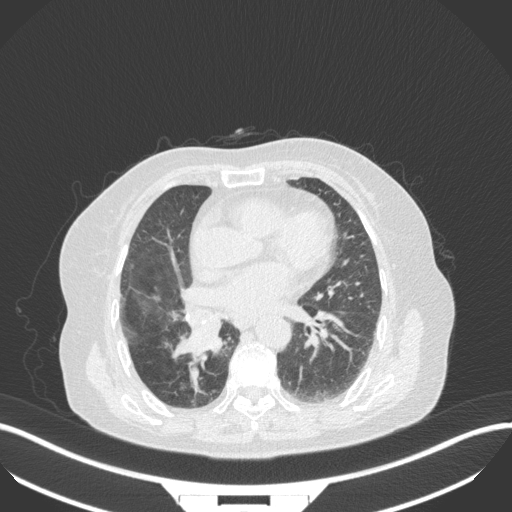
Chest CT, one axial slice. Slice 144 of 329 in the series (ordered by position). Lung window (W 1500 / L -600 HU). 1 mm slice thickness. 512 × 512 image matrix, field of view 400 × 400 mm. Patient: female, 75 years. Case-level facts recorded for this patient, not image findings: clinical TNM (as recorded): T1b N0 M1a.
Structures marked on this image (bounding box drawn by a radiologist):
- lung tumour (recorded histology: squamous cell carcinoma): bounding box [x1, y1, x2, y2] px = [171, 312, 222, 359]